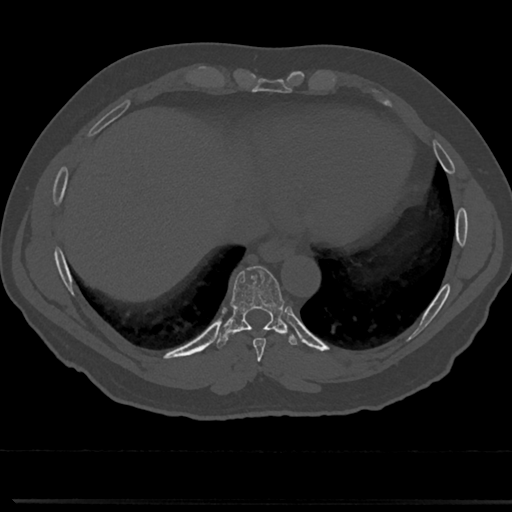
CT including the spine, one axial slice. Slice 320 of 817 in the series (ordered by position). 120 kVp. Bone window (W 1800 / L 400 HU). 512 × 512 image matrix. Patient: male, 61 years. From the clinical record (not read from this slice): primary cancer: prostate.
Structures marked on this image (semi-automatic segmentation, software-assisted and operator-edited):
- T7 vertebra: bounding box (x1, y1, x2, y2) in pixels: (258, 361, 266, 376)
- T8 vertebra: (215, 268, 307, 356)